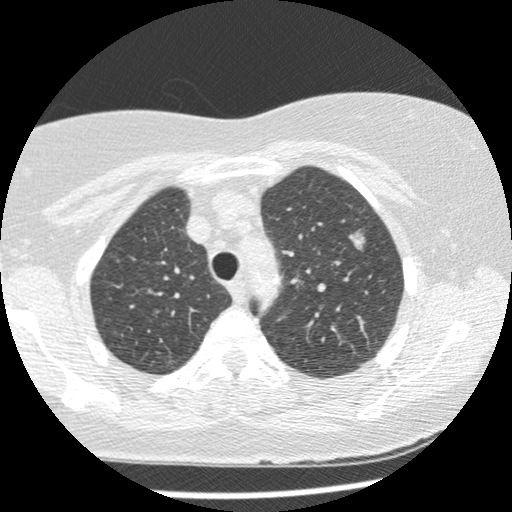
Low-dose screening chest CT, one axial slice; slice 182 of 241 in the series (ordered by position); reconstruction kernel STANDARD; 120 kVp; lung window (W 1500 / L -600 HU); 512 × 512 image matrix, field of view 305 × 305 mm.
Outlined on this slice (expert manual segmentation):
- lesion 2 (tumor, upper lobe of left lung): box from (x=349, y=229) to (x=366, y=251) px